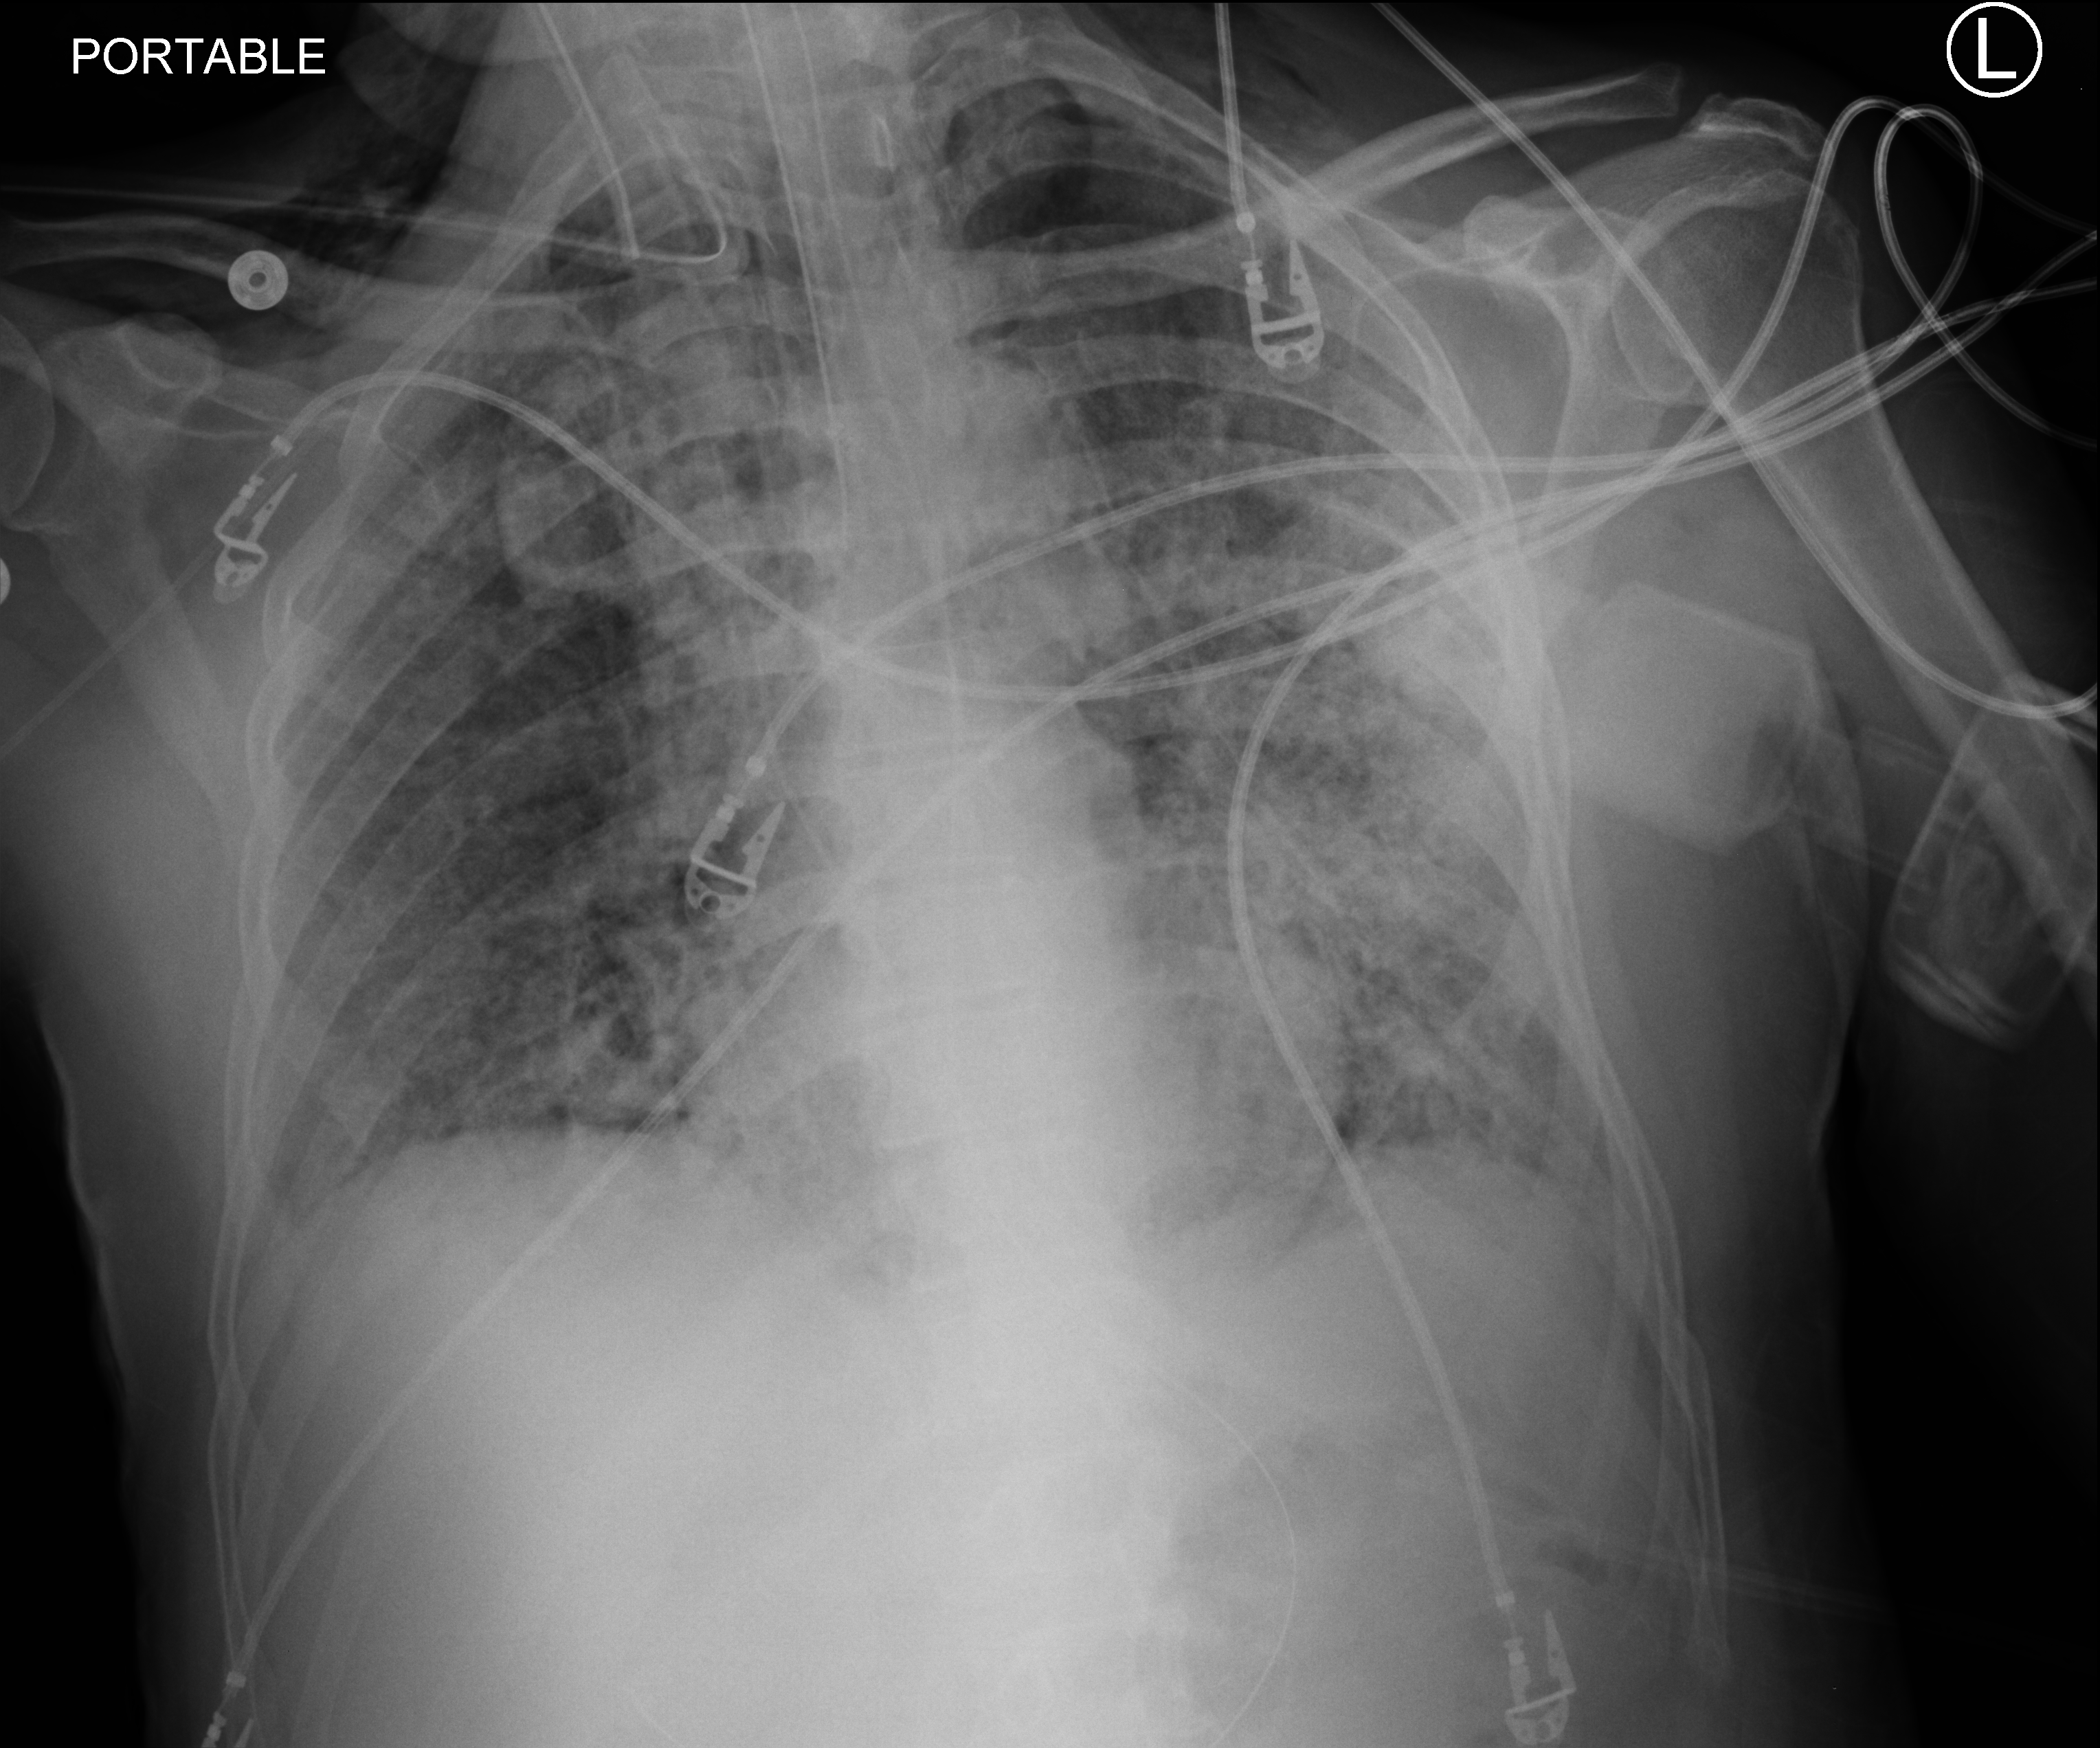
Portable chest radiograph; anteroposterior (AP) projection. Male patient hospitalised with COVID-19, age 60–74 years.
Hospital-stay facts (about this admission, not read from this image; timing relative to this image not recorded): chronic kidney disease (admission record): no; length of hospital stay: 65 days.